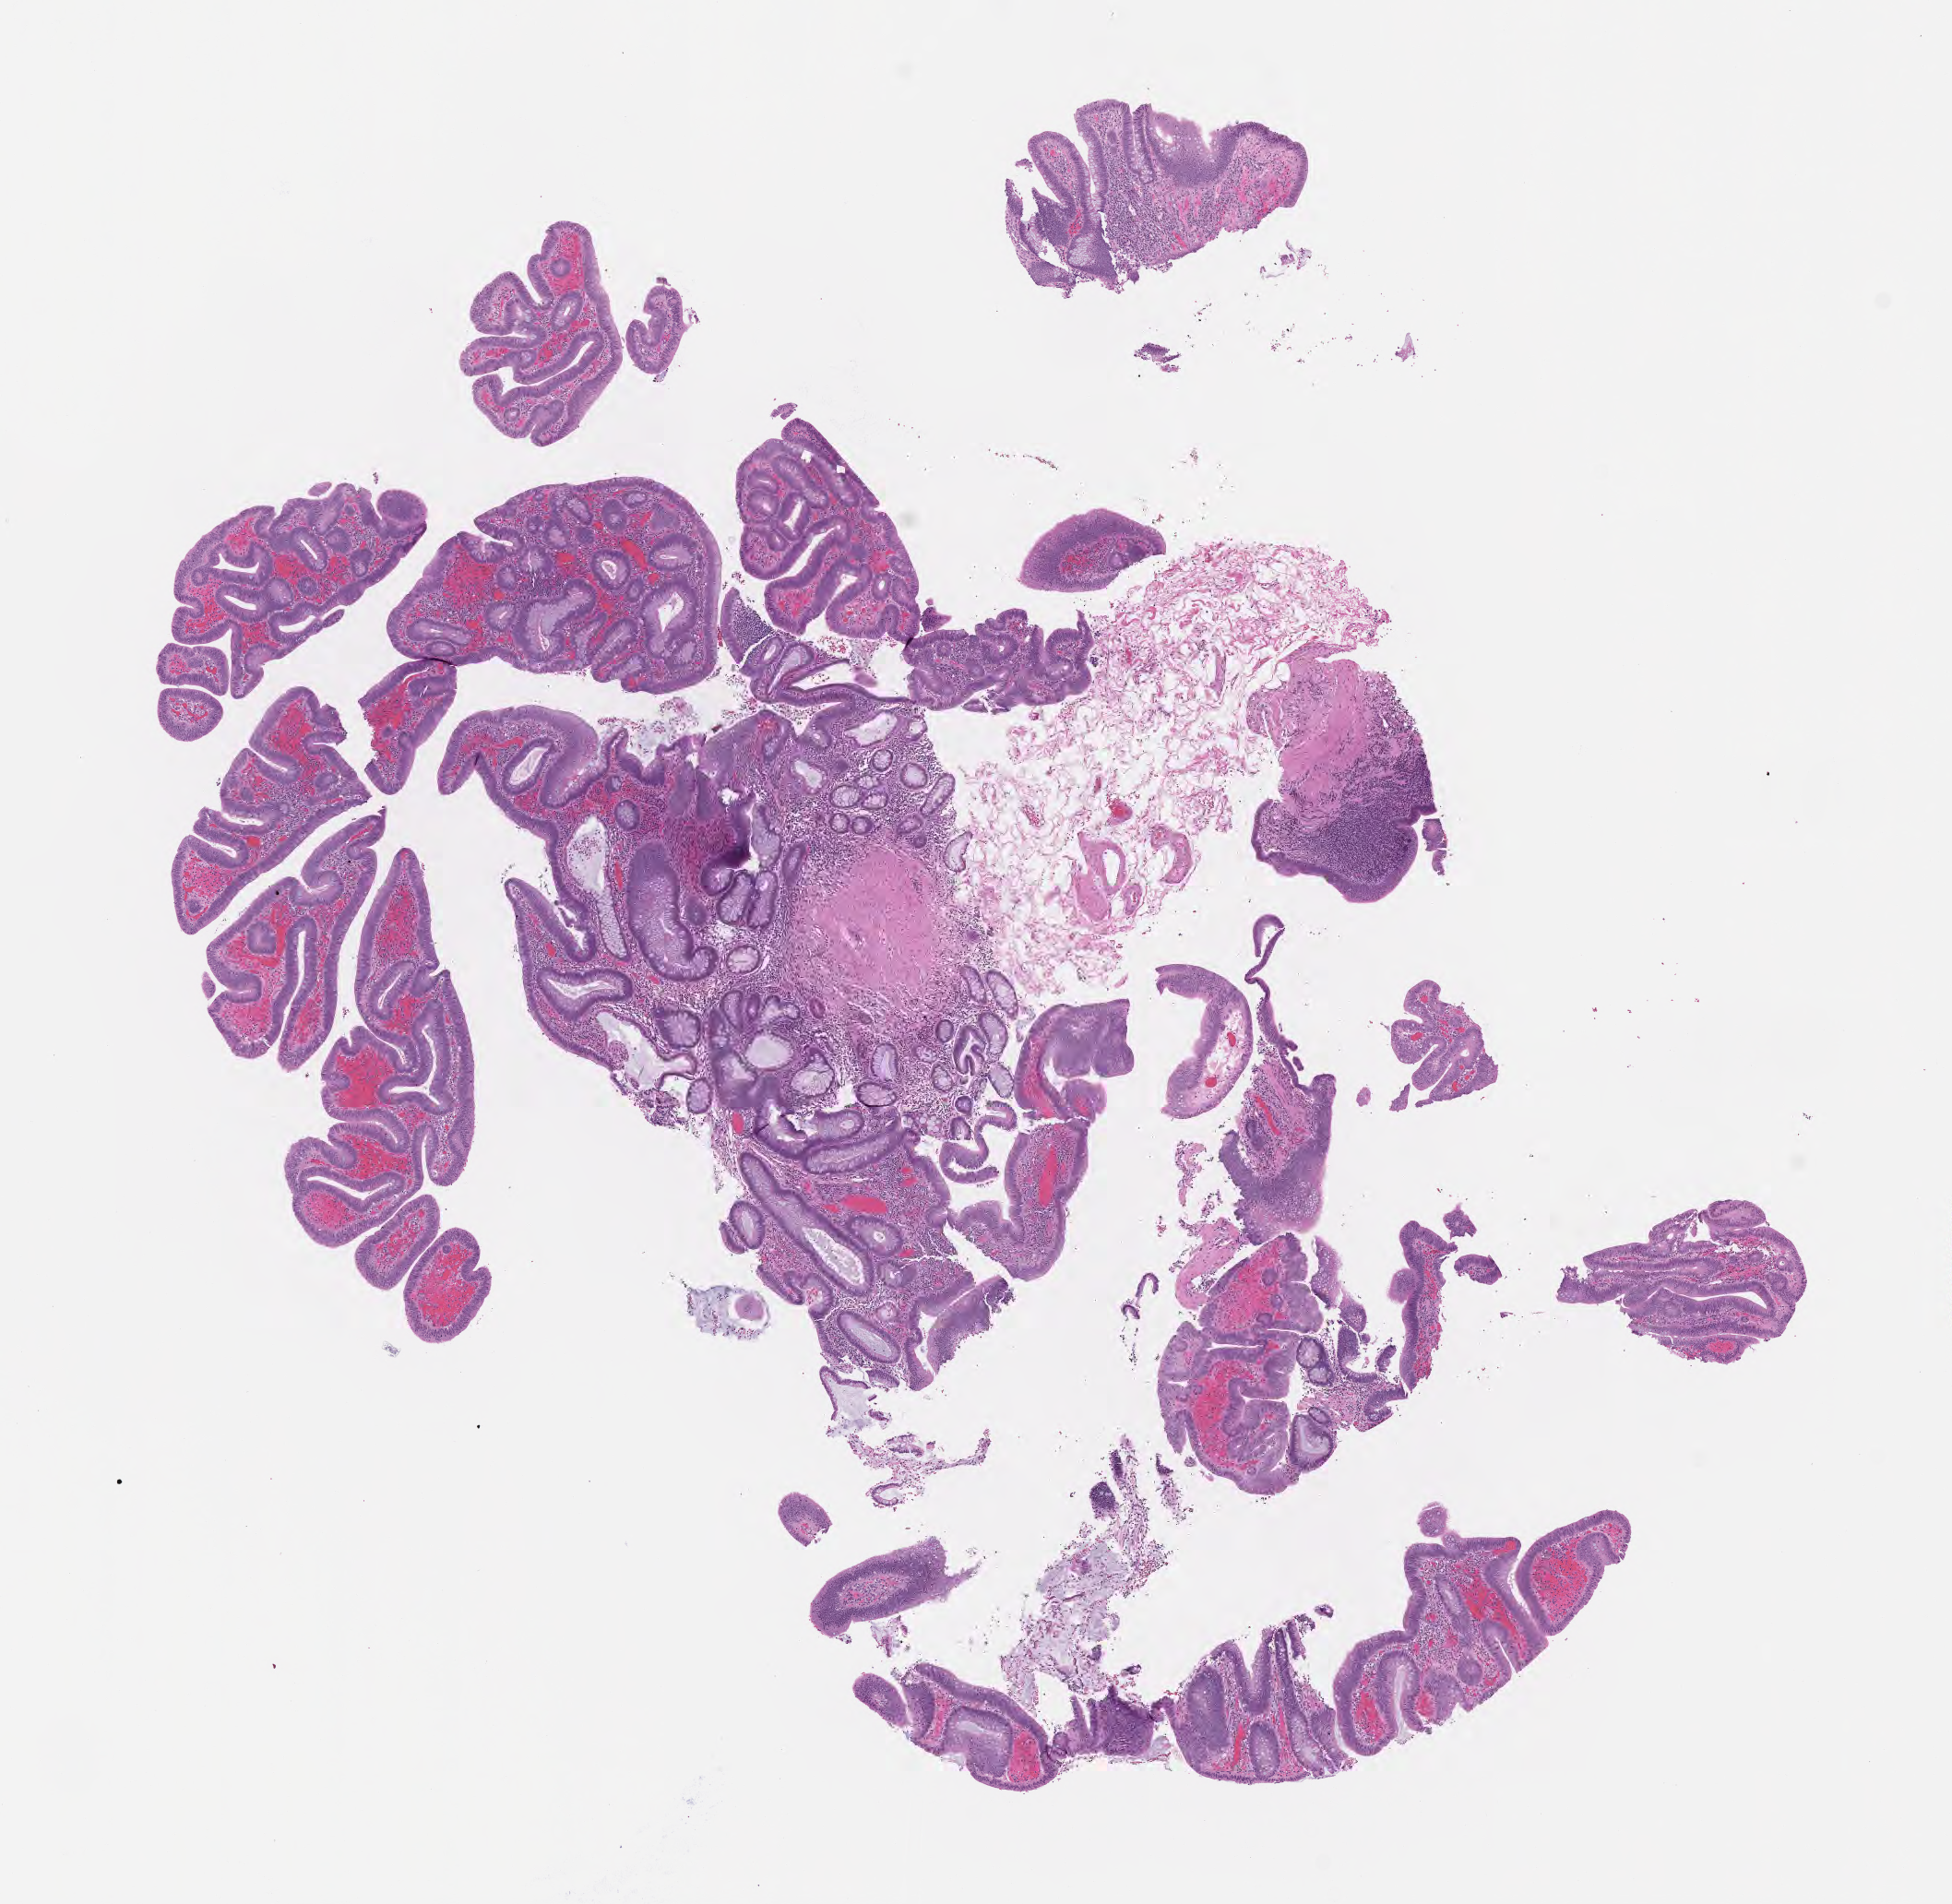
Whole-slide image, H&E stain — shown as a low-resolution overview of the whole scanned area (about 8.6 x 8.3 mm), FFPE section, premalignant lesion from a patient with tubulovillous adenoma, NOS, anatomic site: cecum. Male, age 51 years at initial diagnosis. Composition of this section per pathologist review: tumor cells 75%, tumor nuclei 75%, stromal cells 25%, necrosis 0%, normal cells 0%. Infiltration values recorded for this section: lymphocyte infiltration 5%, monocyte infiltration 2%, neutrophil infiltration 12%.
This section: sample classed premalignant; the patient's recorded diagnosis is given above. Section: top of the tissue portion.